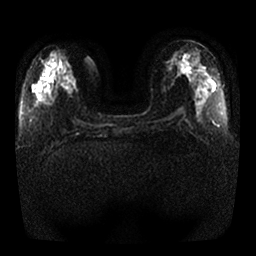
Breast MRI, one axial slice; slice 10 of 25 in the series (ordered by position); diffusion-weighted series; image 2 of 4 stored at this slice position (different b-values; order by instance number); 1.5 T; 256 × 256 image matrix. Female patient.
Annotated regions visible in this slice (expert manual segmentation):
- tumour on diffusion-weighted imaging: bounding box (x1, y1, x2, y2) in pixels: (70, 76, 76, 87)